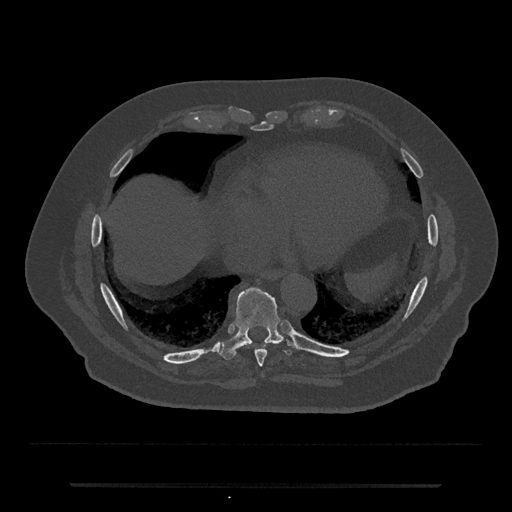
CT including the spine, one axial slice. Slice 775 of 797 in the series (ordered by position). 120 kVp. Bone window (W 1800 / L 400 HU). 0.5 mm slice thickness. 512 × 512 image matrix, field of view 434 × 434 mm. Patient: male, 80 years. From the clinical record (not read from this slice): primary cancer: prostate.
Structures marked on this image (semi-automatic segmentation, software-assisted and operator-edited):
- T8 vertebra: bounding box <255,350,267,367> (left, top, right, bottom; pixels)
- T9 vertebra: <217,287,298,360>